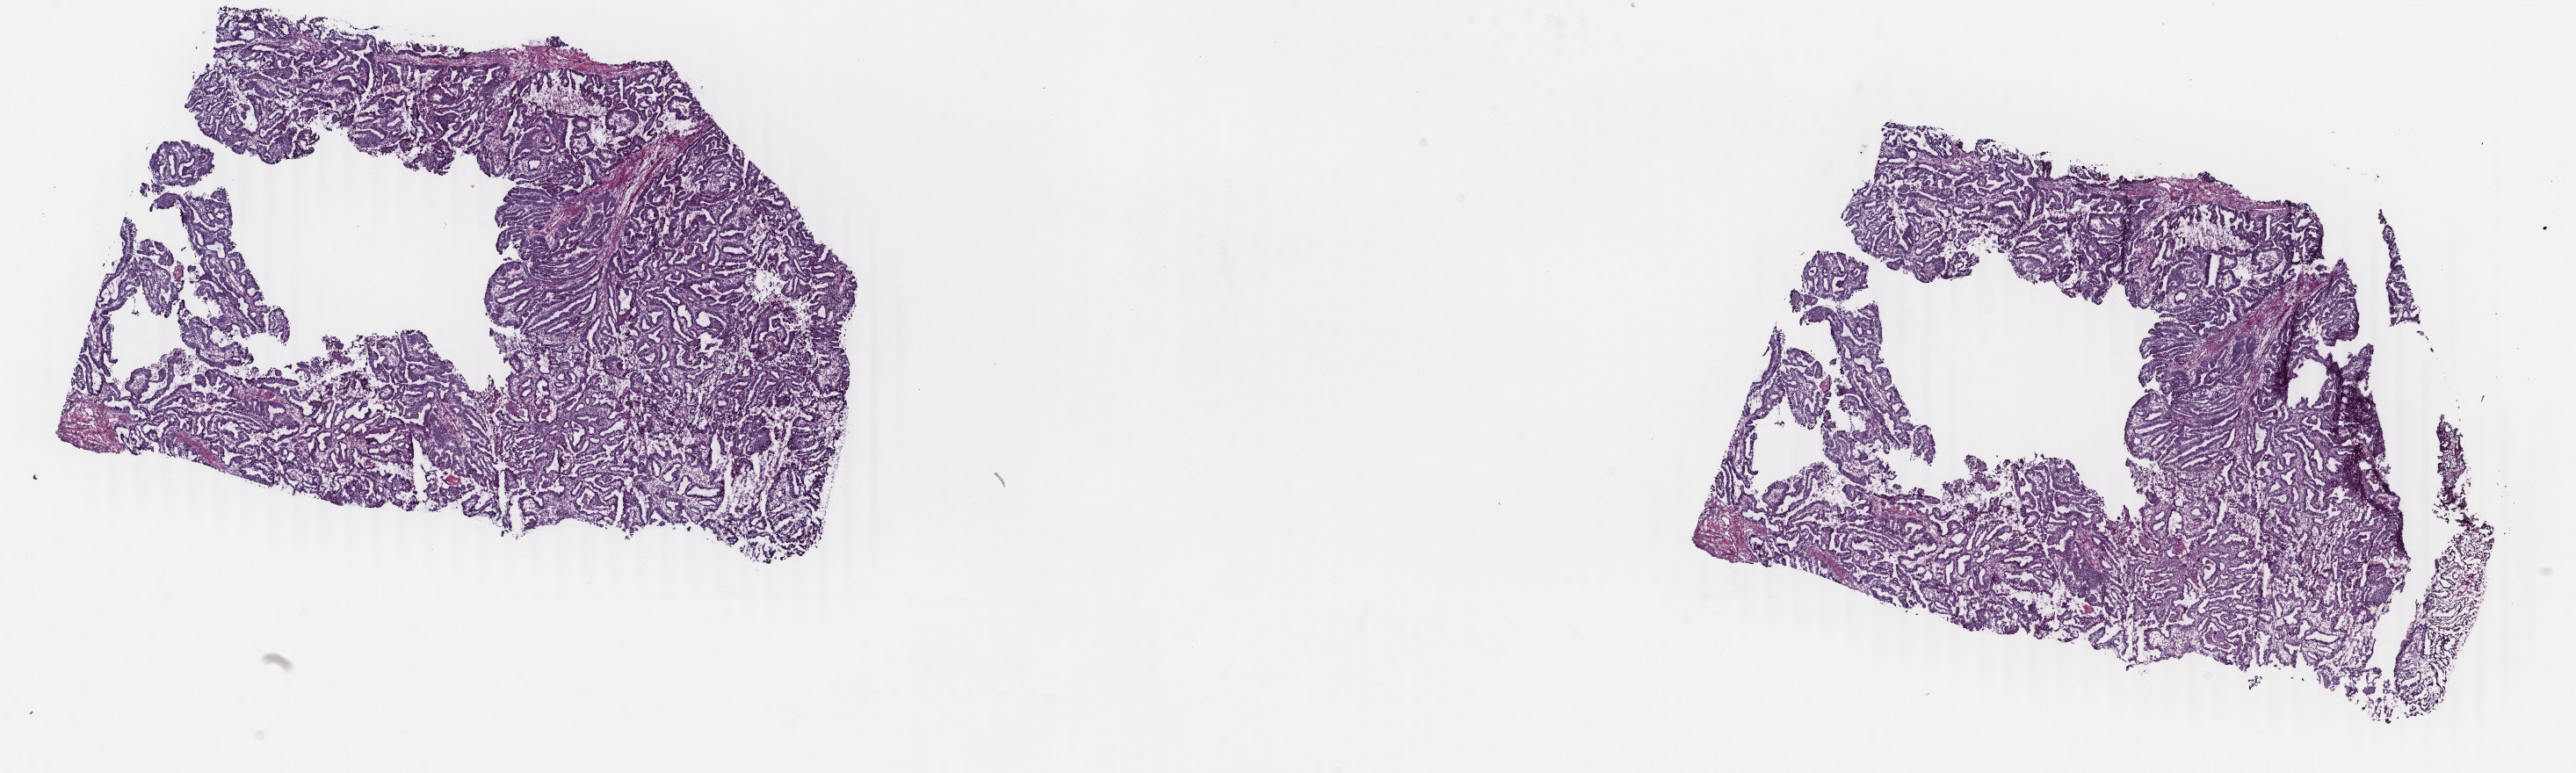
H&E whole-slide image, a low-resolution overview of the entire scanned area, about 23.3 x 7.0 mm. Frozen section. Primary tumour sample from the uterus. Female, age 64 years at initial diagnosis. Histologic grade: G1 (well differentiated). Slide review estimates, as recorded: tumour cells 70%, tumour nuclei 80%, normal cells 10%, stromal cells 10%, necrosis 10%. Inflammatory infiltration, as recorded: lymphocyte infiltration 10%, monocyte infiltration 0%, neutrophil infiltration 0%.
- pathologic diagnosis: Endometrioid adenocarcinoma, NOS (endometrium)
- FIGO stage: IA